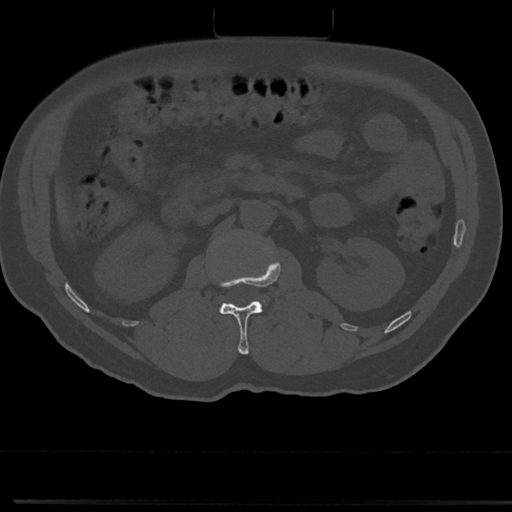
CT including the spine, one axial slice. Slice 59 of 817 in the series (ordered by position). 120 kVp. Bone window (W 1800 / L 400 HU). 0.5 mm slice thickness. 512 × 512 image matrix. Patient: male, 61 years. Case-level facts recorded for this patient, not image findings: primary cancer: prostate.
Outlined on this slice (semi-automatic segmentation, software-assisted and operator-edited):
- L1 vertebra: bounding box (x1, y1, x2, y2) in pixels: (214, 257, 280, 354)